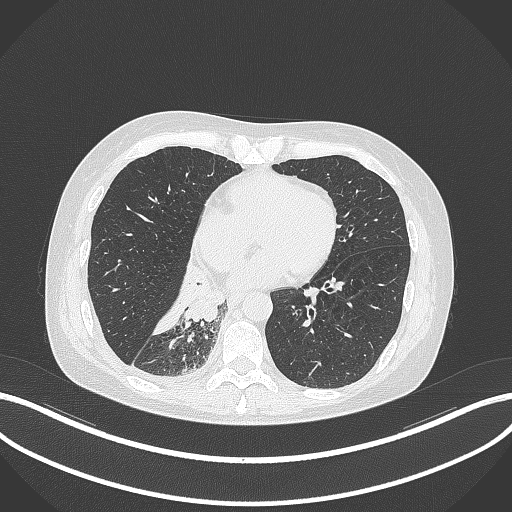
Chest CT, one axial slice. Position 114 of 329 along the scan axis. Reconstruction kernel B70f. Lung window (W 1500 / L -600 HU). 1 mm slice thickness. 512 × 512 image matrix, field of view 400 × 400 mm. Patient: female, 63 years. Case-level facts recorded for this patient, not image findings: clinical TNM (as recorded): T1c N0 M0.
Structures marked on this image (bounding box drawn by a radiologist):
- lung tumour (recorded histology: adenocarcinoma): box from (x=178, y=264) to (x=228, y=325) px